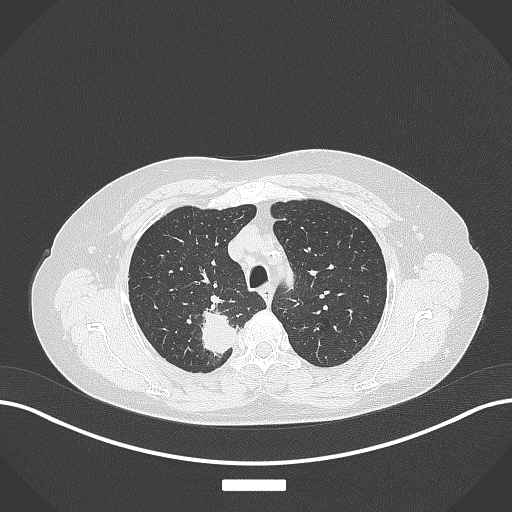
Chest CT, one axial slice. Position 301 of 357 along the scan axis. Lung window (W 1500 / L -600 HU). 1 mm slice thickness. 512 × 512 image matrix, field of view 400 × 400 mm. Patient: female, 62 years. Case-level facts recorded for this patient, not image findings: clinical TNM (as recorded): T1c N1 M0.
Annotated regions visible in this slice (rectangle marked by the reading radiologist):
- lung tumour (recorded histology: squamous cell carcinoma): bounding box [x1, y1, x2, y2] px = [198, 303, 246, 356]